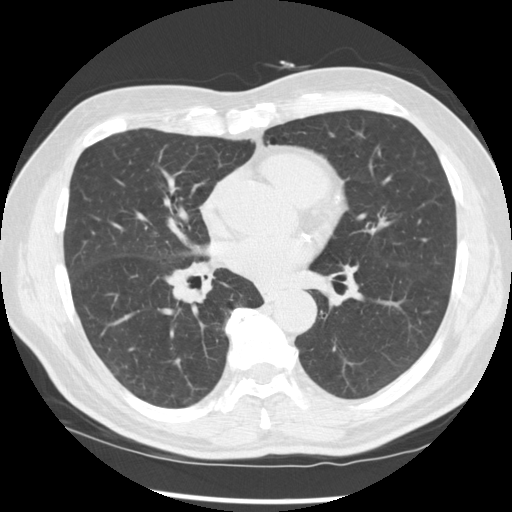
Low-dose screening chest CT, one axial slice. Slice 137 of 277 in the series (ordered by position). Lung window (W 1500 / L -600 HU). 512 × 512 image matrix, field of view 365 × 365 mm.
Structures marked on this image (expert manual segmentation):
- lesion 1 (tumor, middle lobe of right lung): bounding box (x1, y1, x2, y2) in pixels: (166, 270, 206, 304)